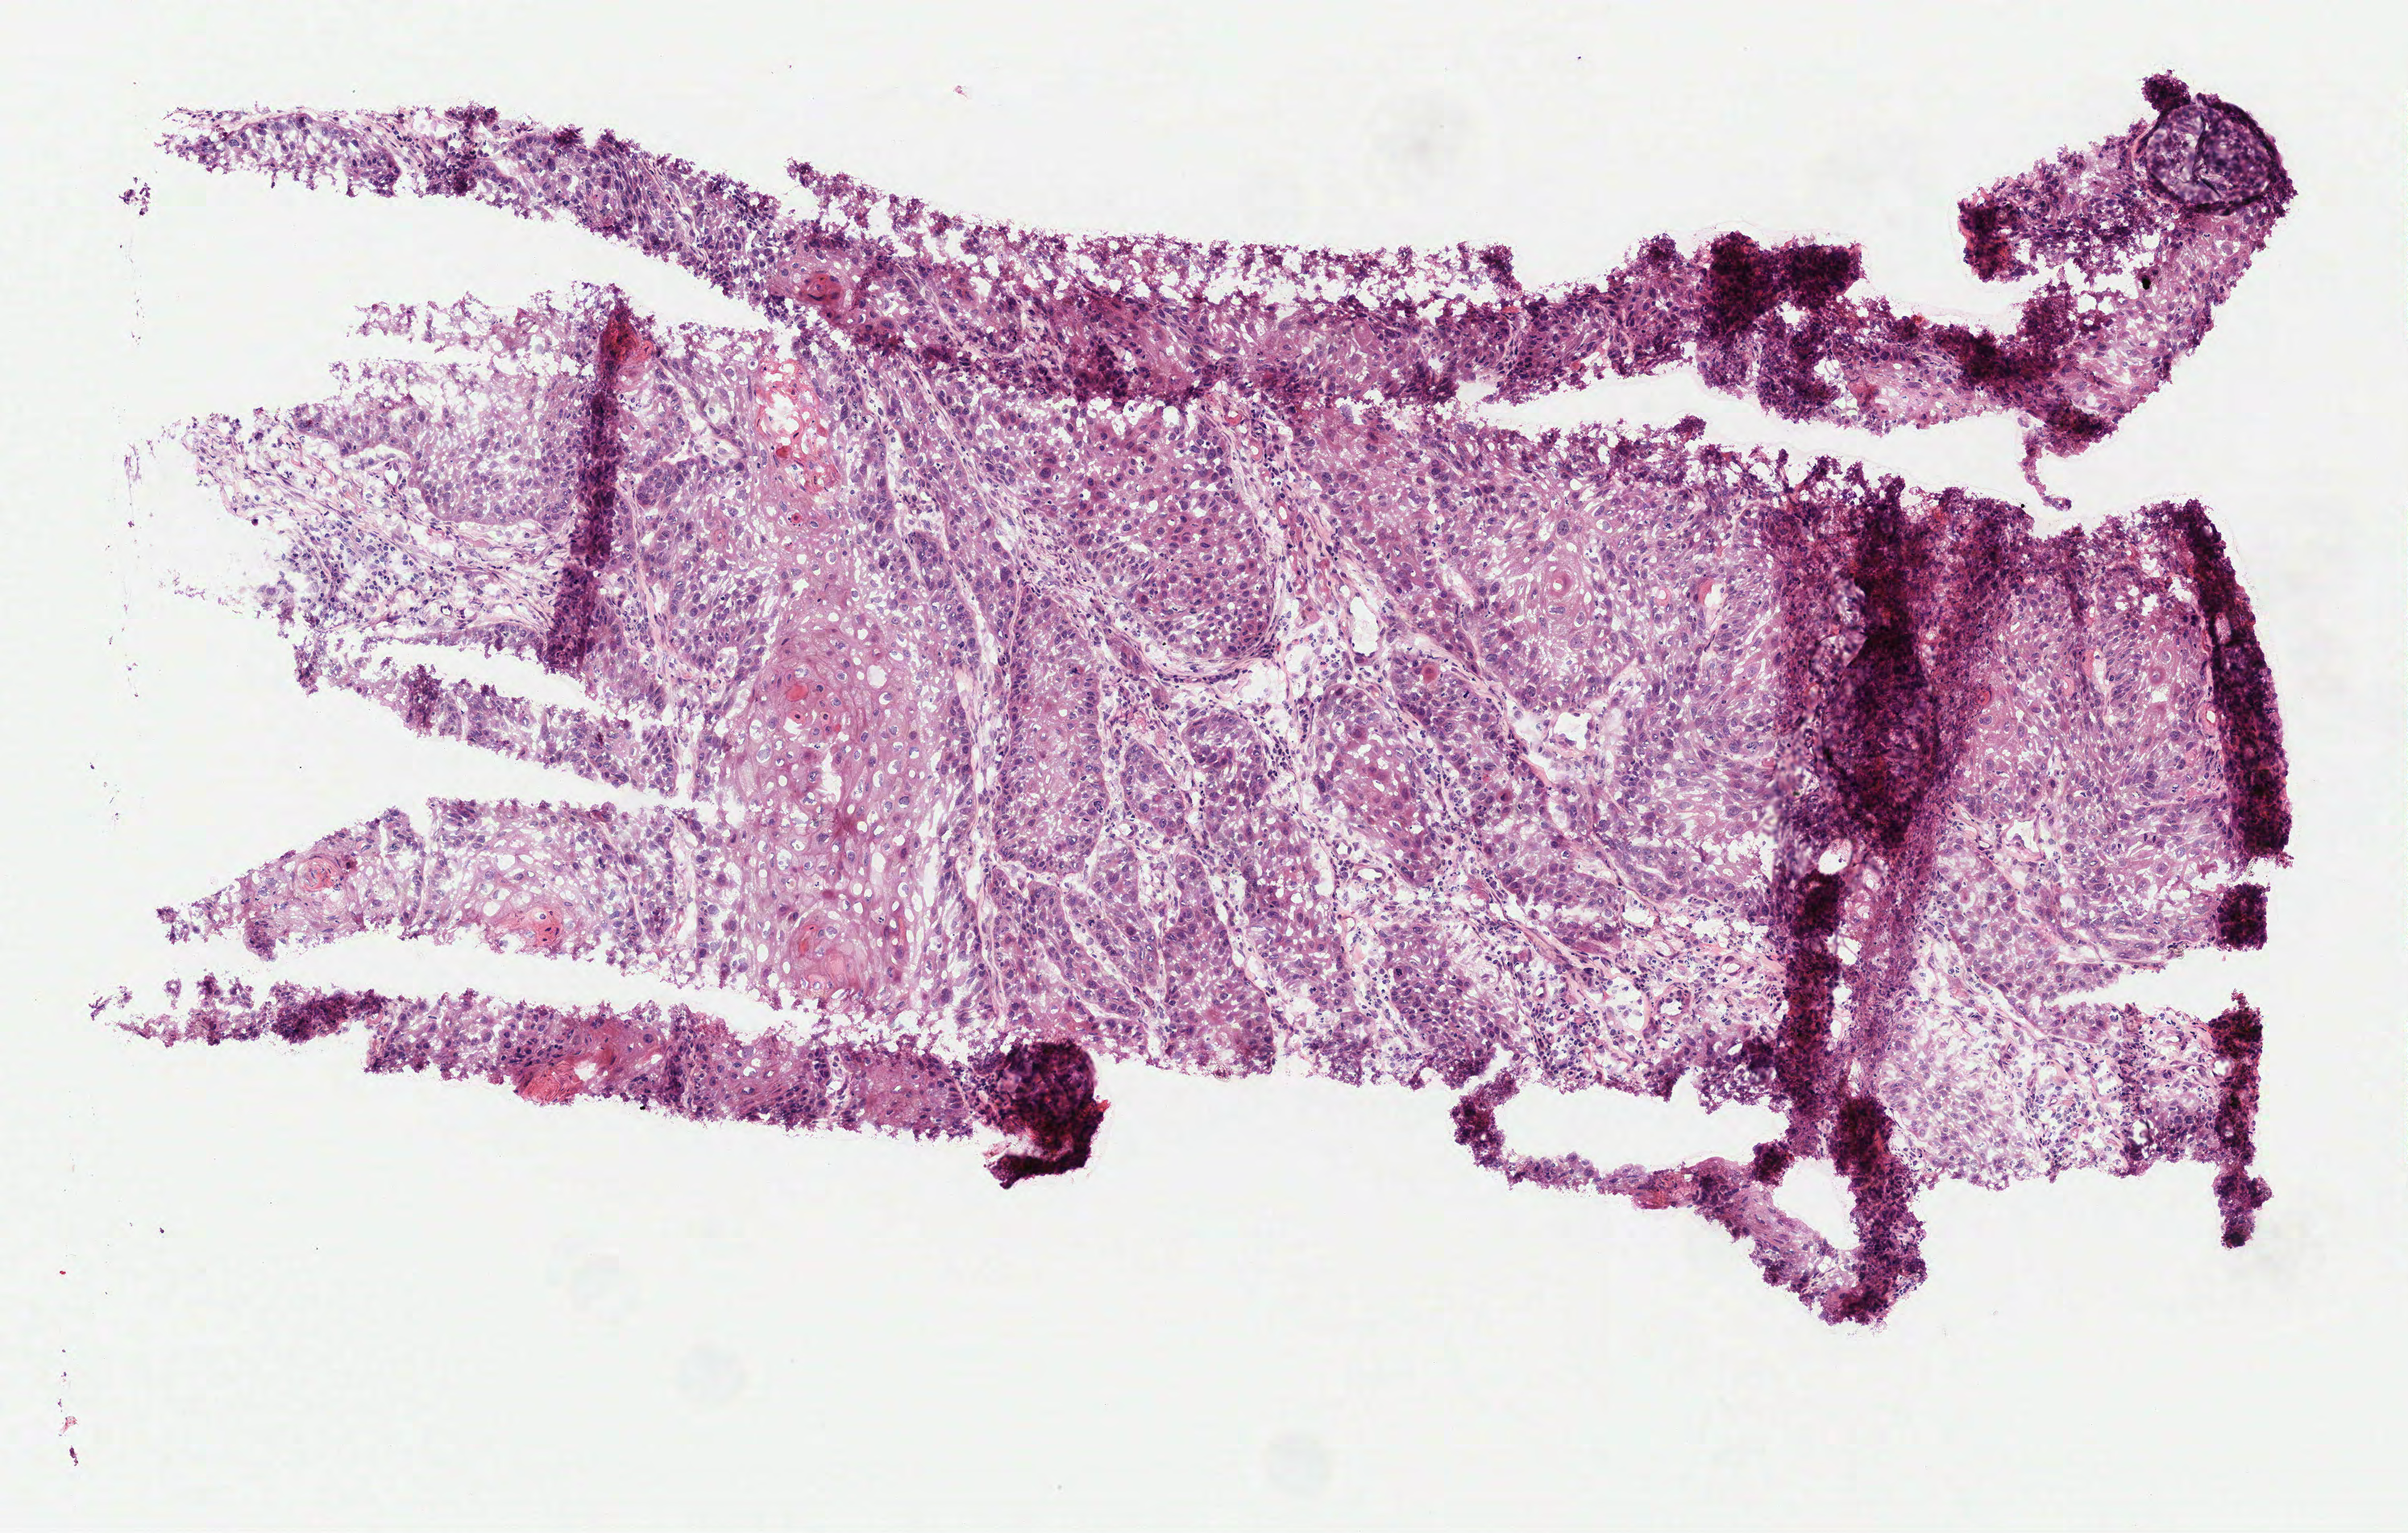
H&E whole-slide image, low-resolution overview of the scanned area, about 3.0 x 1.9 mm (acquisition: 40x scan). Frozen section from the top of the tissue portion. Primary tumour sample from the head and neck. Patient: male, age at initial diagnosis 52 years. Histologic grade: G2 (moderately differentiated). Slide review estimates, as recorded: tumour cells 100%, tumour nuclei 85%, normal cells 0%, stromal cells 0%, necrosis 0%. Inflammatory infiltration, as recorded: lymphocyte infiltration 10%, monocyte infiltration 0%, neutrophil infiltration 4%.
- laterality: midline
- diagnosis: Squamous cell carcinoma, keratinizing, NOS (tongue, NOS)
- AJCC pathologic stage: II (7th edition)
- TNM: T2 N0 M0